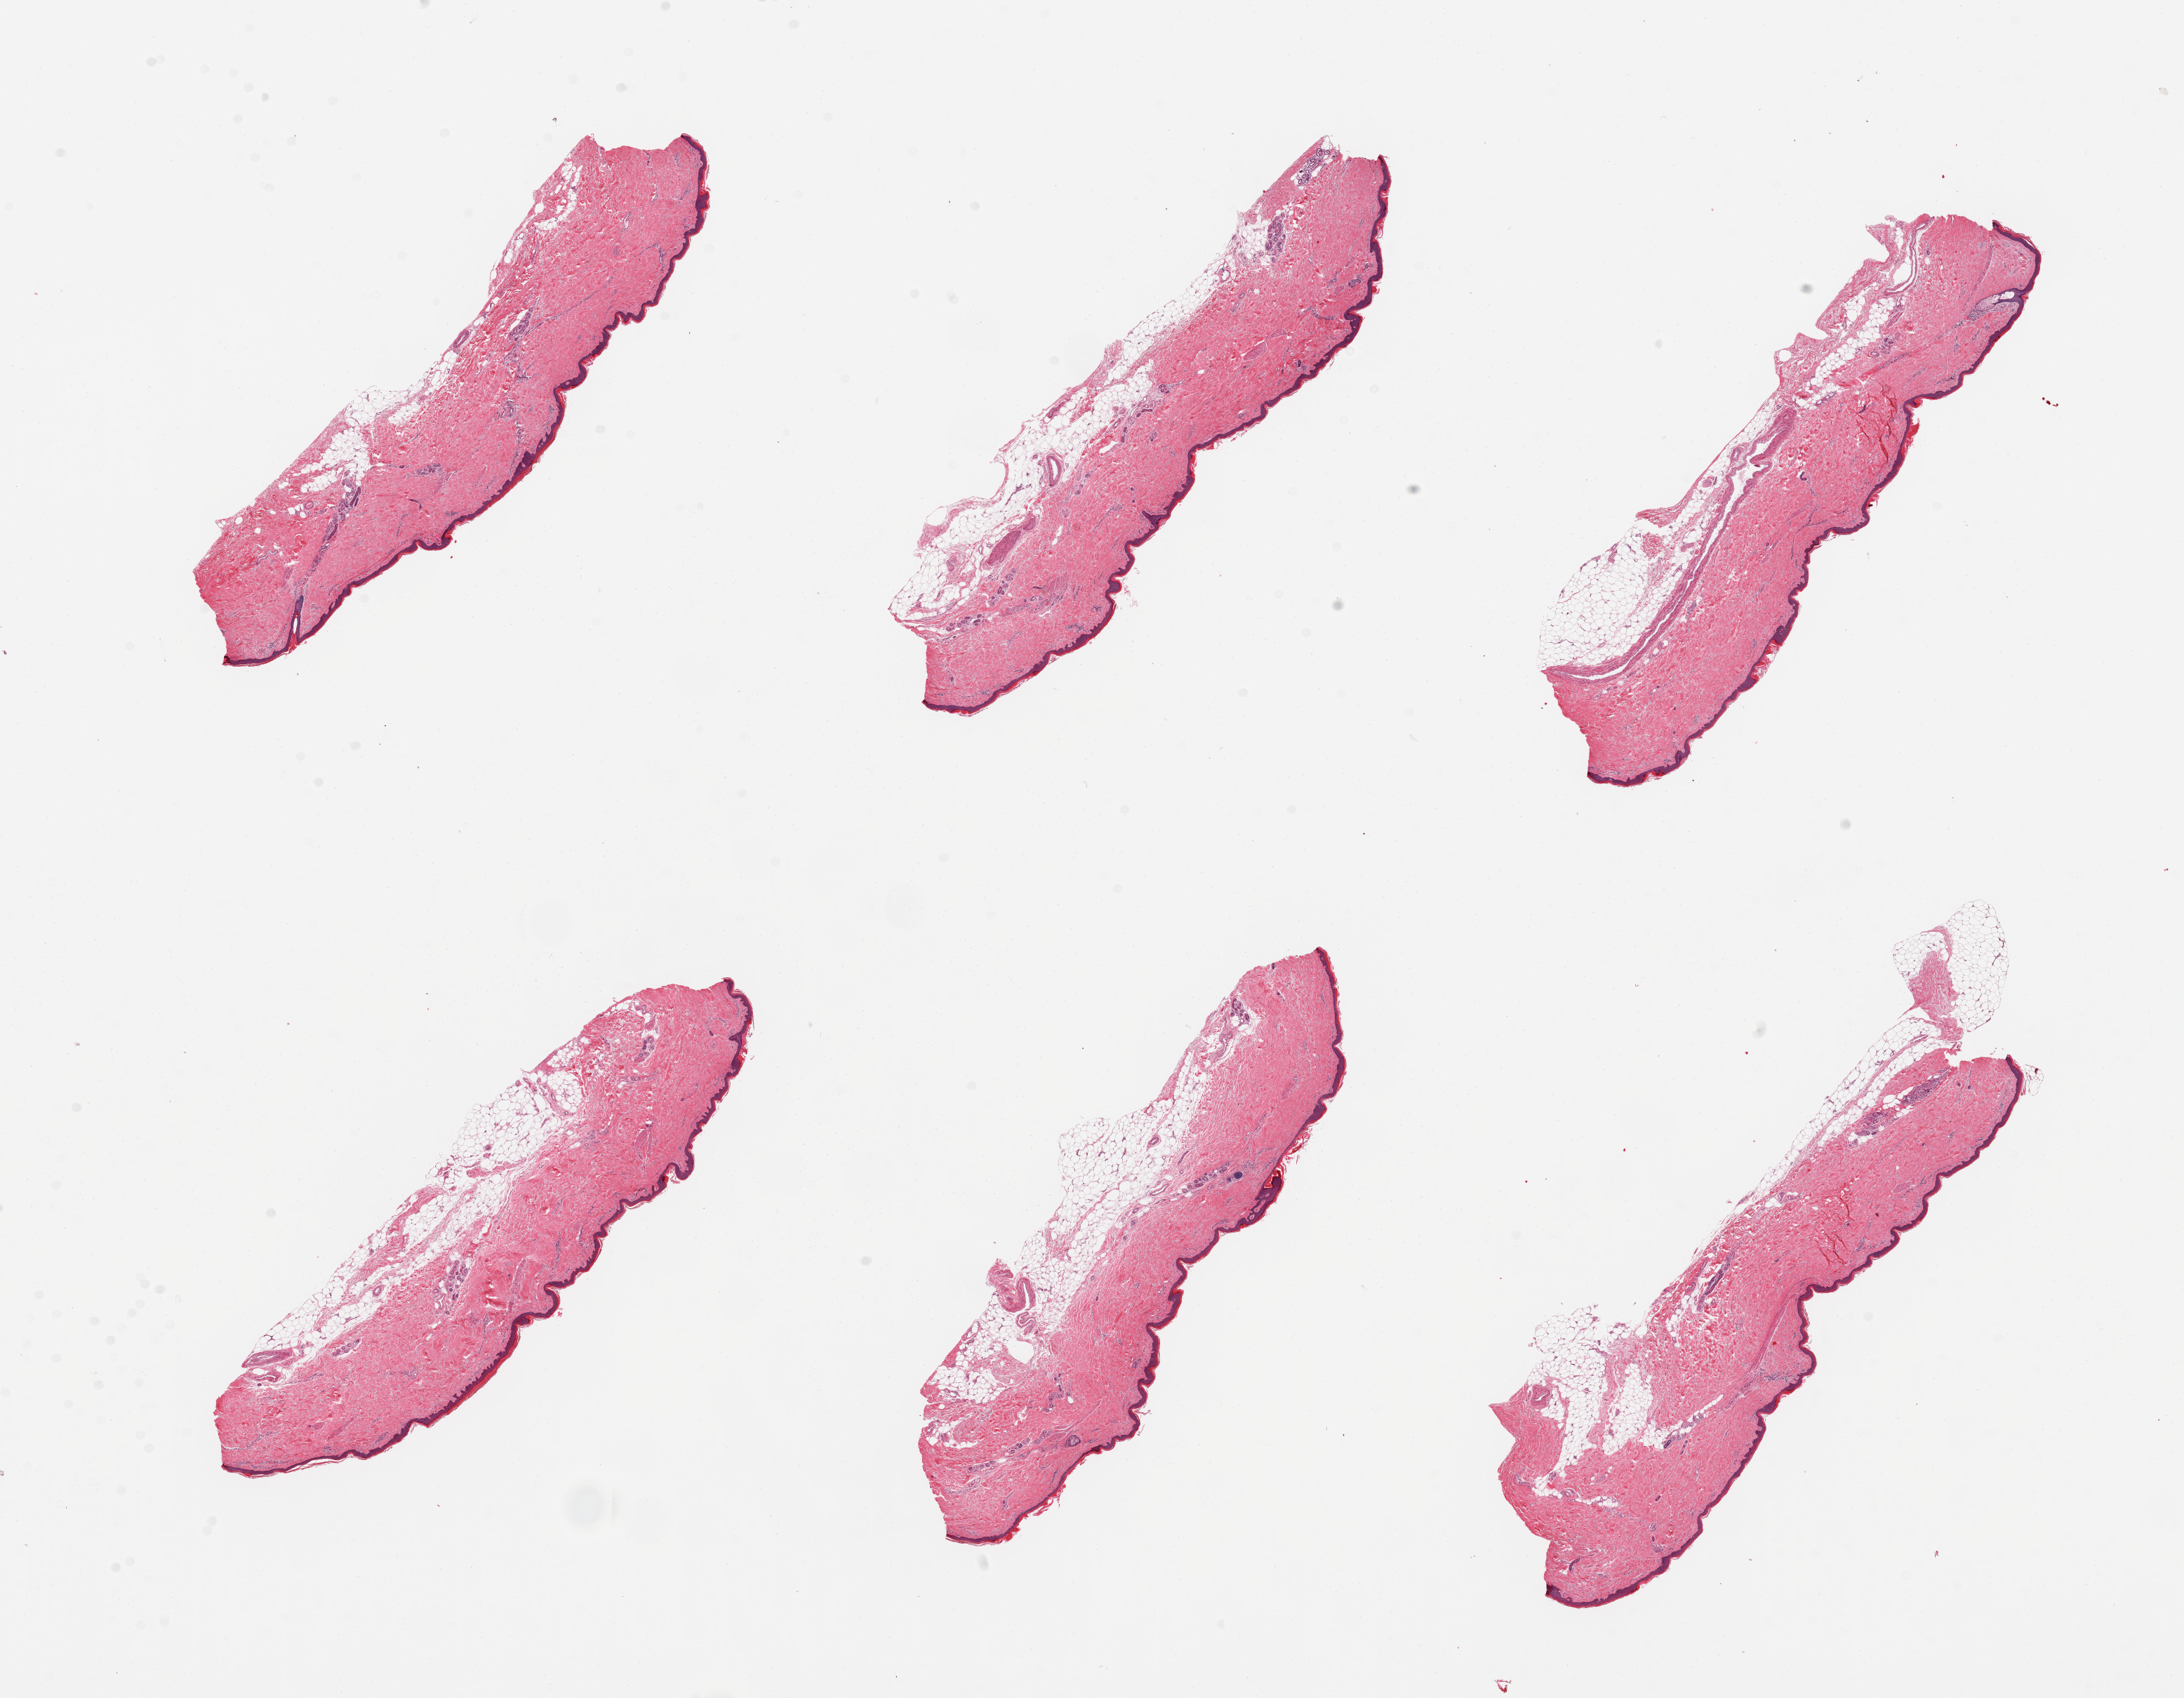
Digitized hematoxylin and eosin (H&E)-stained section — low-resolution overview of the scanned area, about 24.6 x 19.1 mm. PAXgene-fixed, paraffin-embedded tissue. Target tissue: skin of lower leg. Donor tissue sample. Donor sex: male.
Pathologist's review note for this sample: 6 pieces; up to 1 mm subcutaneous fat on all.